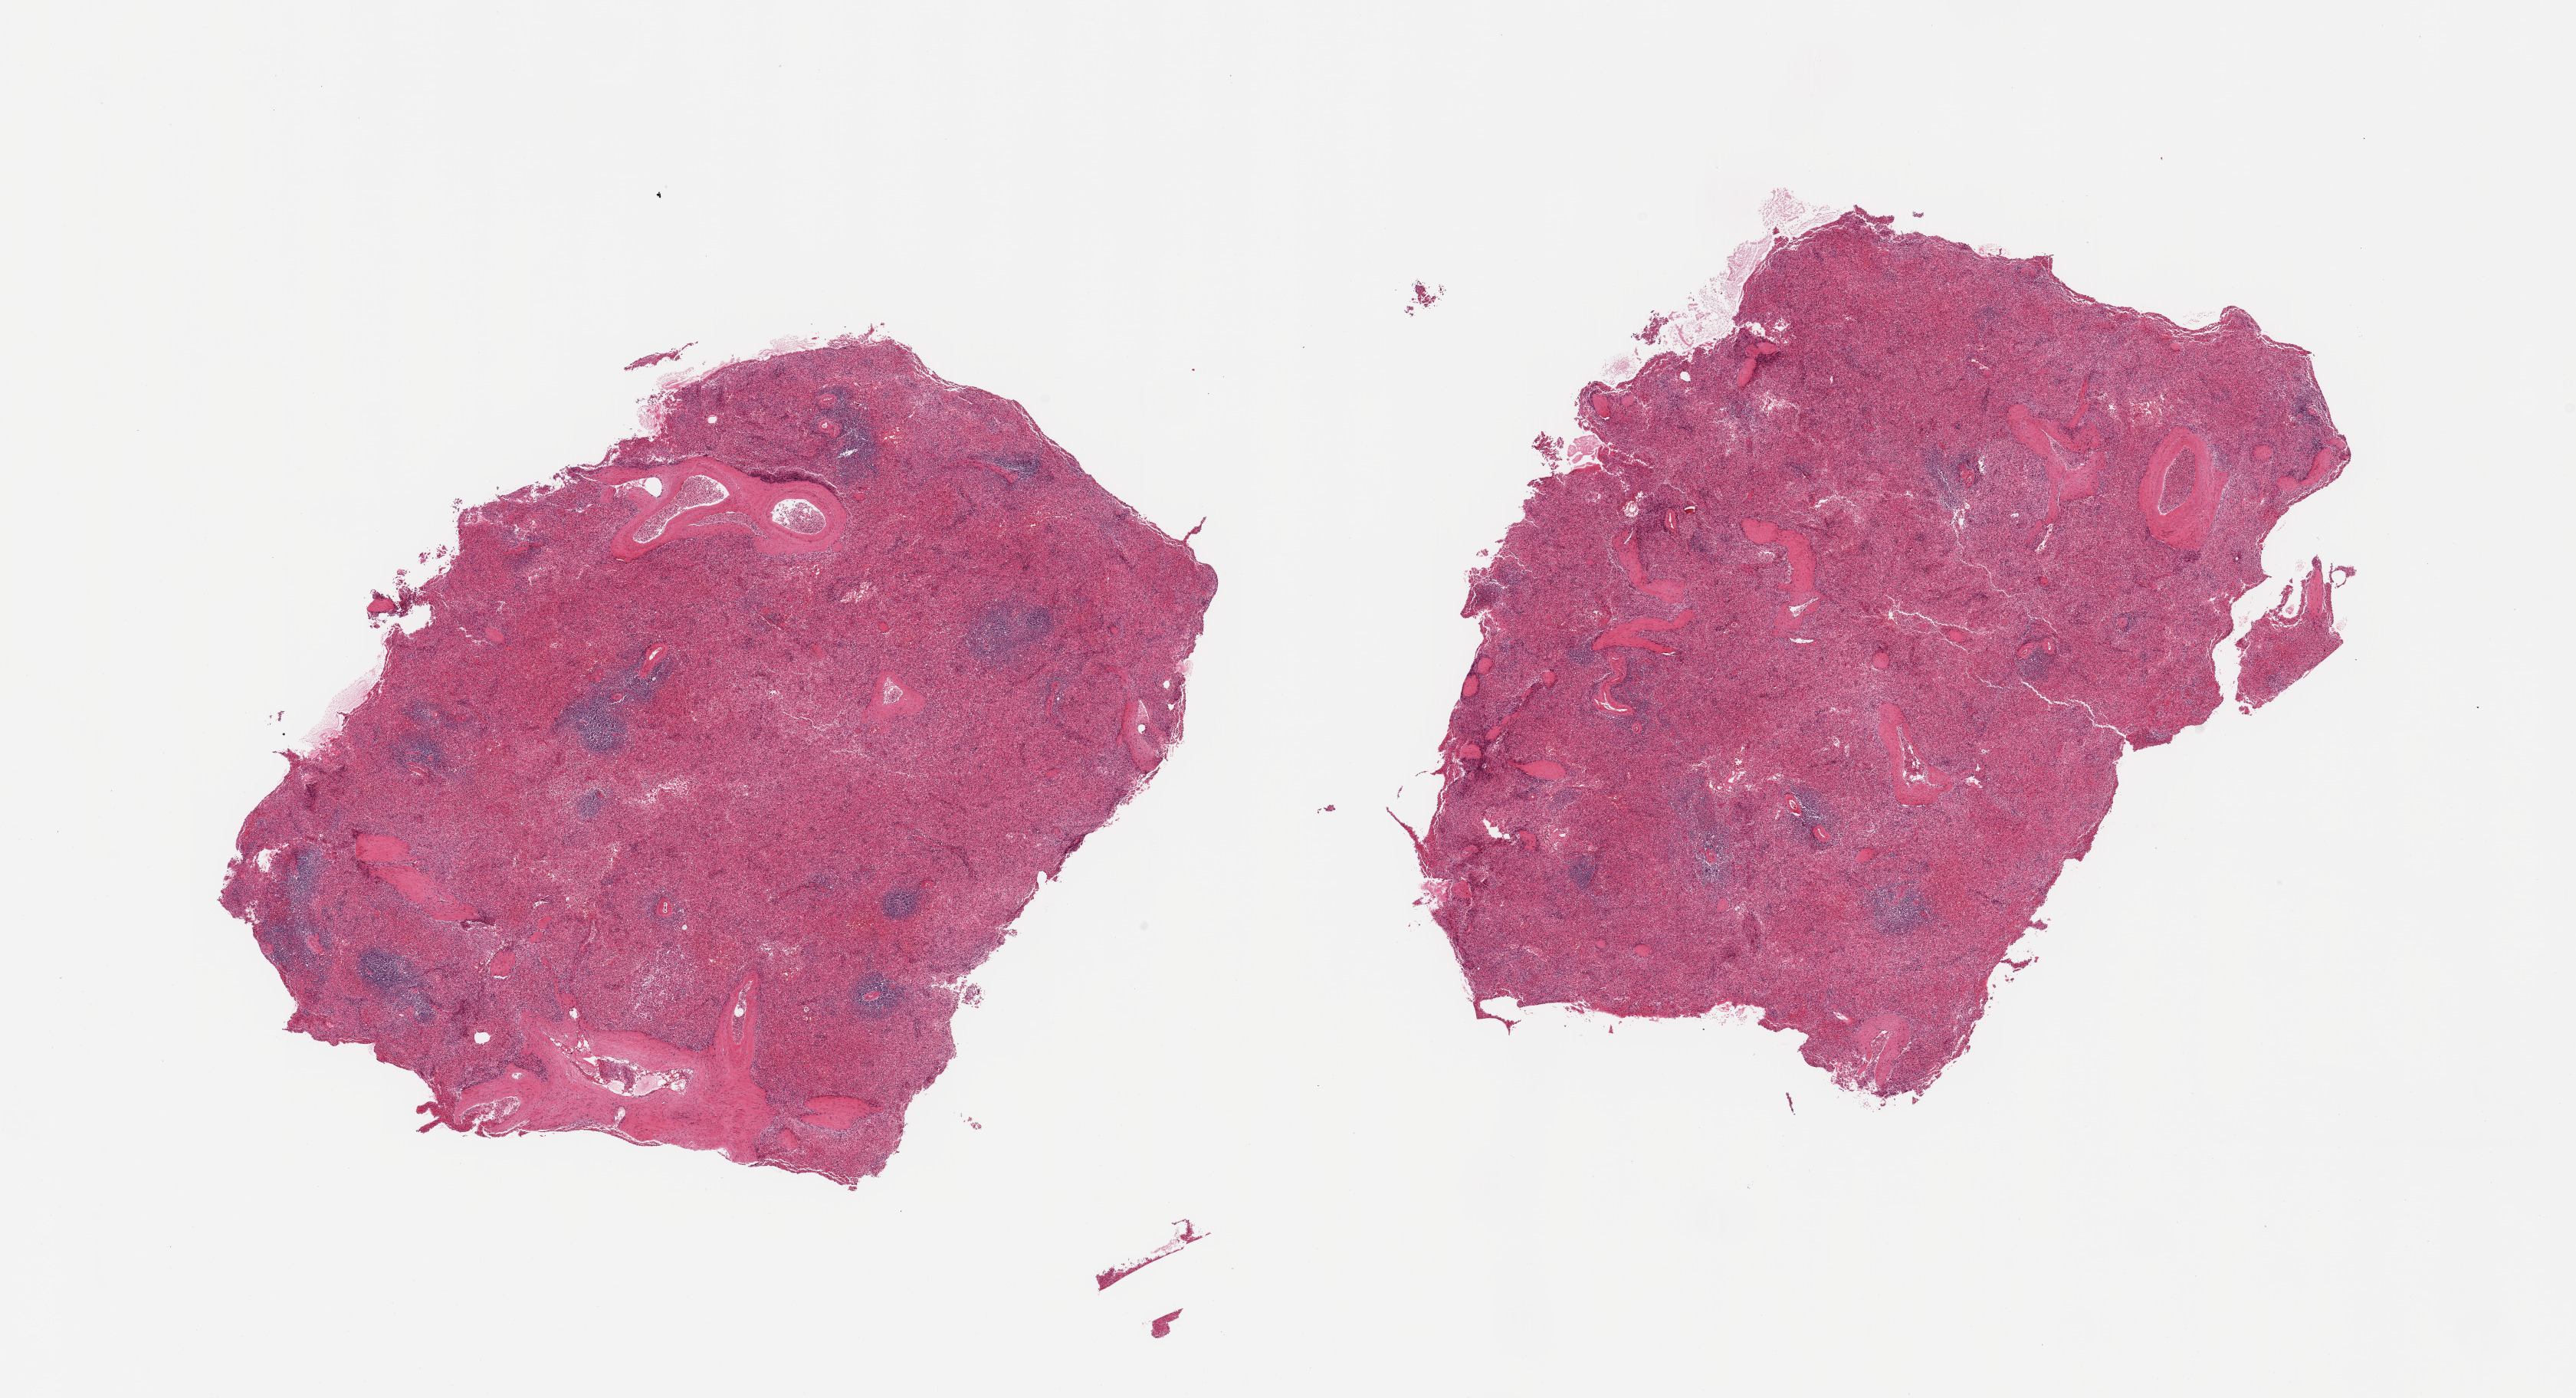
Digitized H&E-stained section, brightfield — low-resolution overview of the scanned area, about 26.6 x 14.4 mm (from a 20x scan); PAXgene-fixed paraffin-embedded (PFPE) section; sampled site (target tissue): spleen; tissue donor sample. Donor sex: male.
Reviewer comment on this tissue sample: 2 pieces.